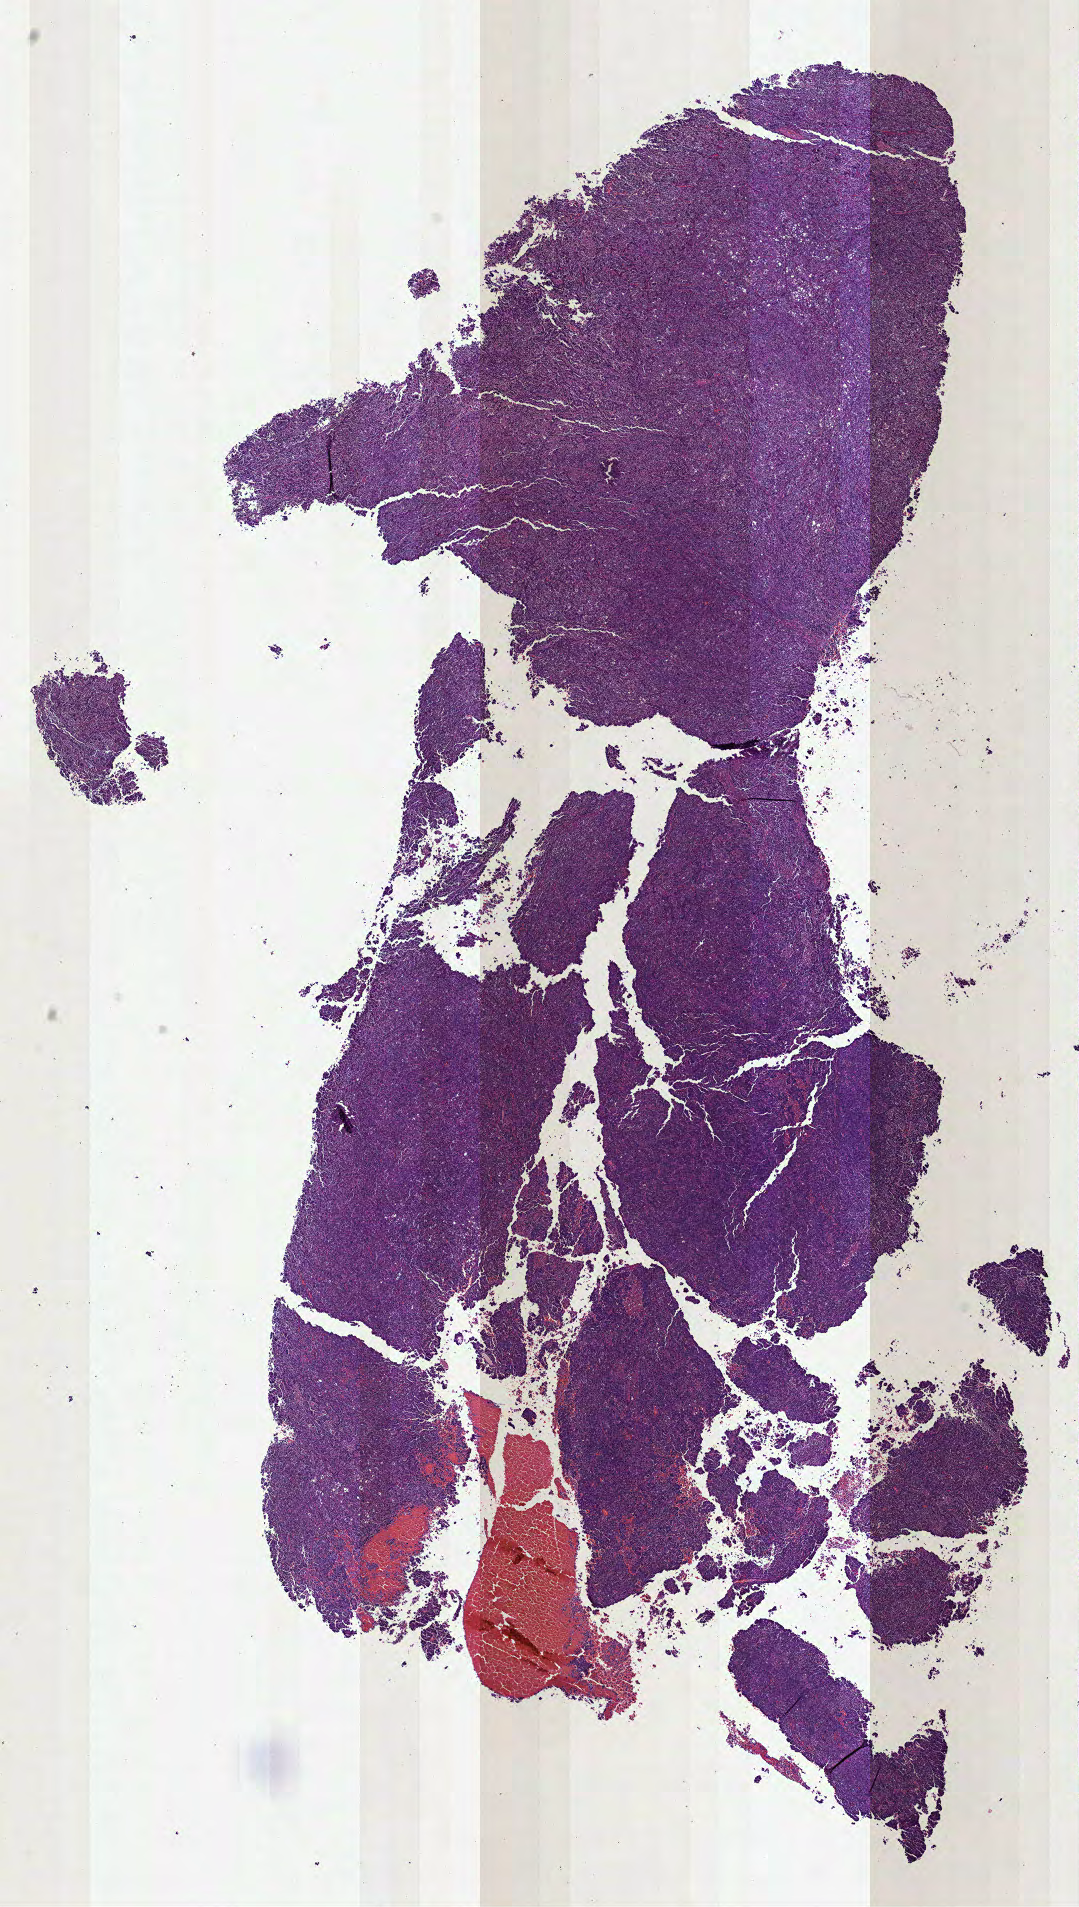
Hematoxylin and eosin (H&E) stained whole-slide image, shown as a low-resolution overview of the whole scanned area (about 8.7 x 15.4 mm, acquisition: 40x scan), formalin-fixed paraffin-embedded (FFPE) diagnostic section, uterus, primary tumour sample. Female patient; age at initial diagnosis 78 years. Histologic grade: G3 (poorly differentiated).
FIGO stage: IB. Diagnosis: Serous cystadenocarcinoma, NOS.